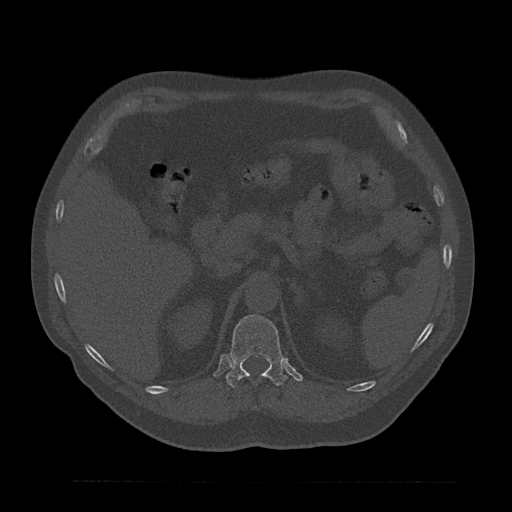
CT including the spine, one axial slice; position 239 of 797 along the scan axis; 120 kVp; bone window (W 1800 / L 400 HU); 0.5 mm slice thickness; 512 × 512 image matrix. Male patient, age 61 years. Case-level facts recorded for this patient, not image findings: primary cancer: prostate.
Outlined on this slice (semi-automatically segmented with operator editing):
- T12 vertebra: bounding box [x1, y1, x2, y2] px = [226, 315, 287, 389]